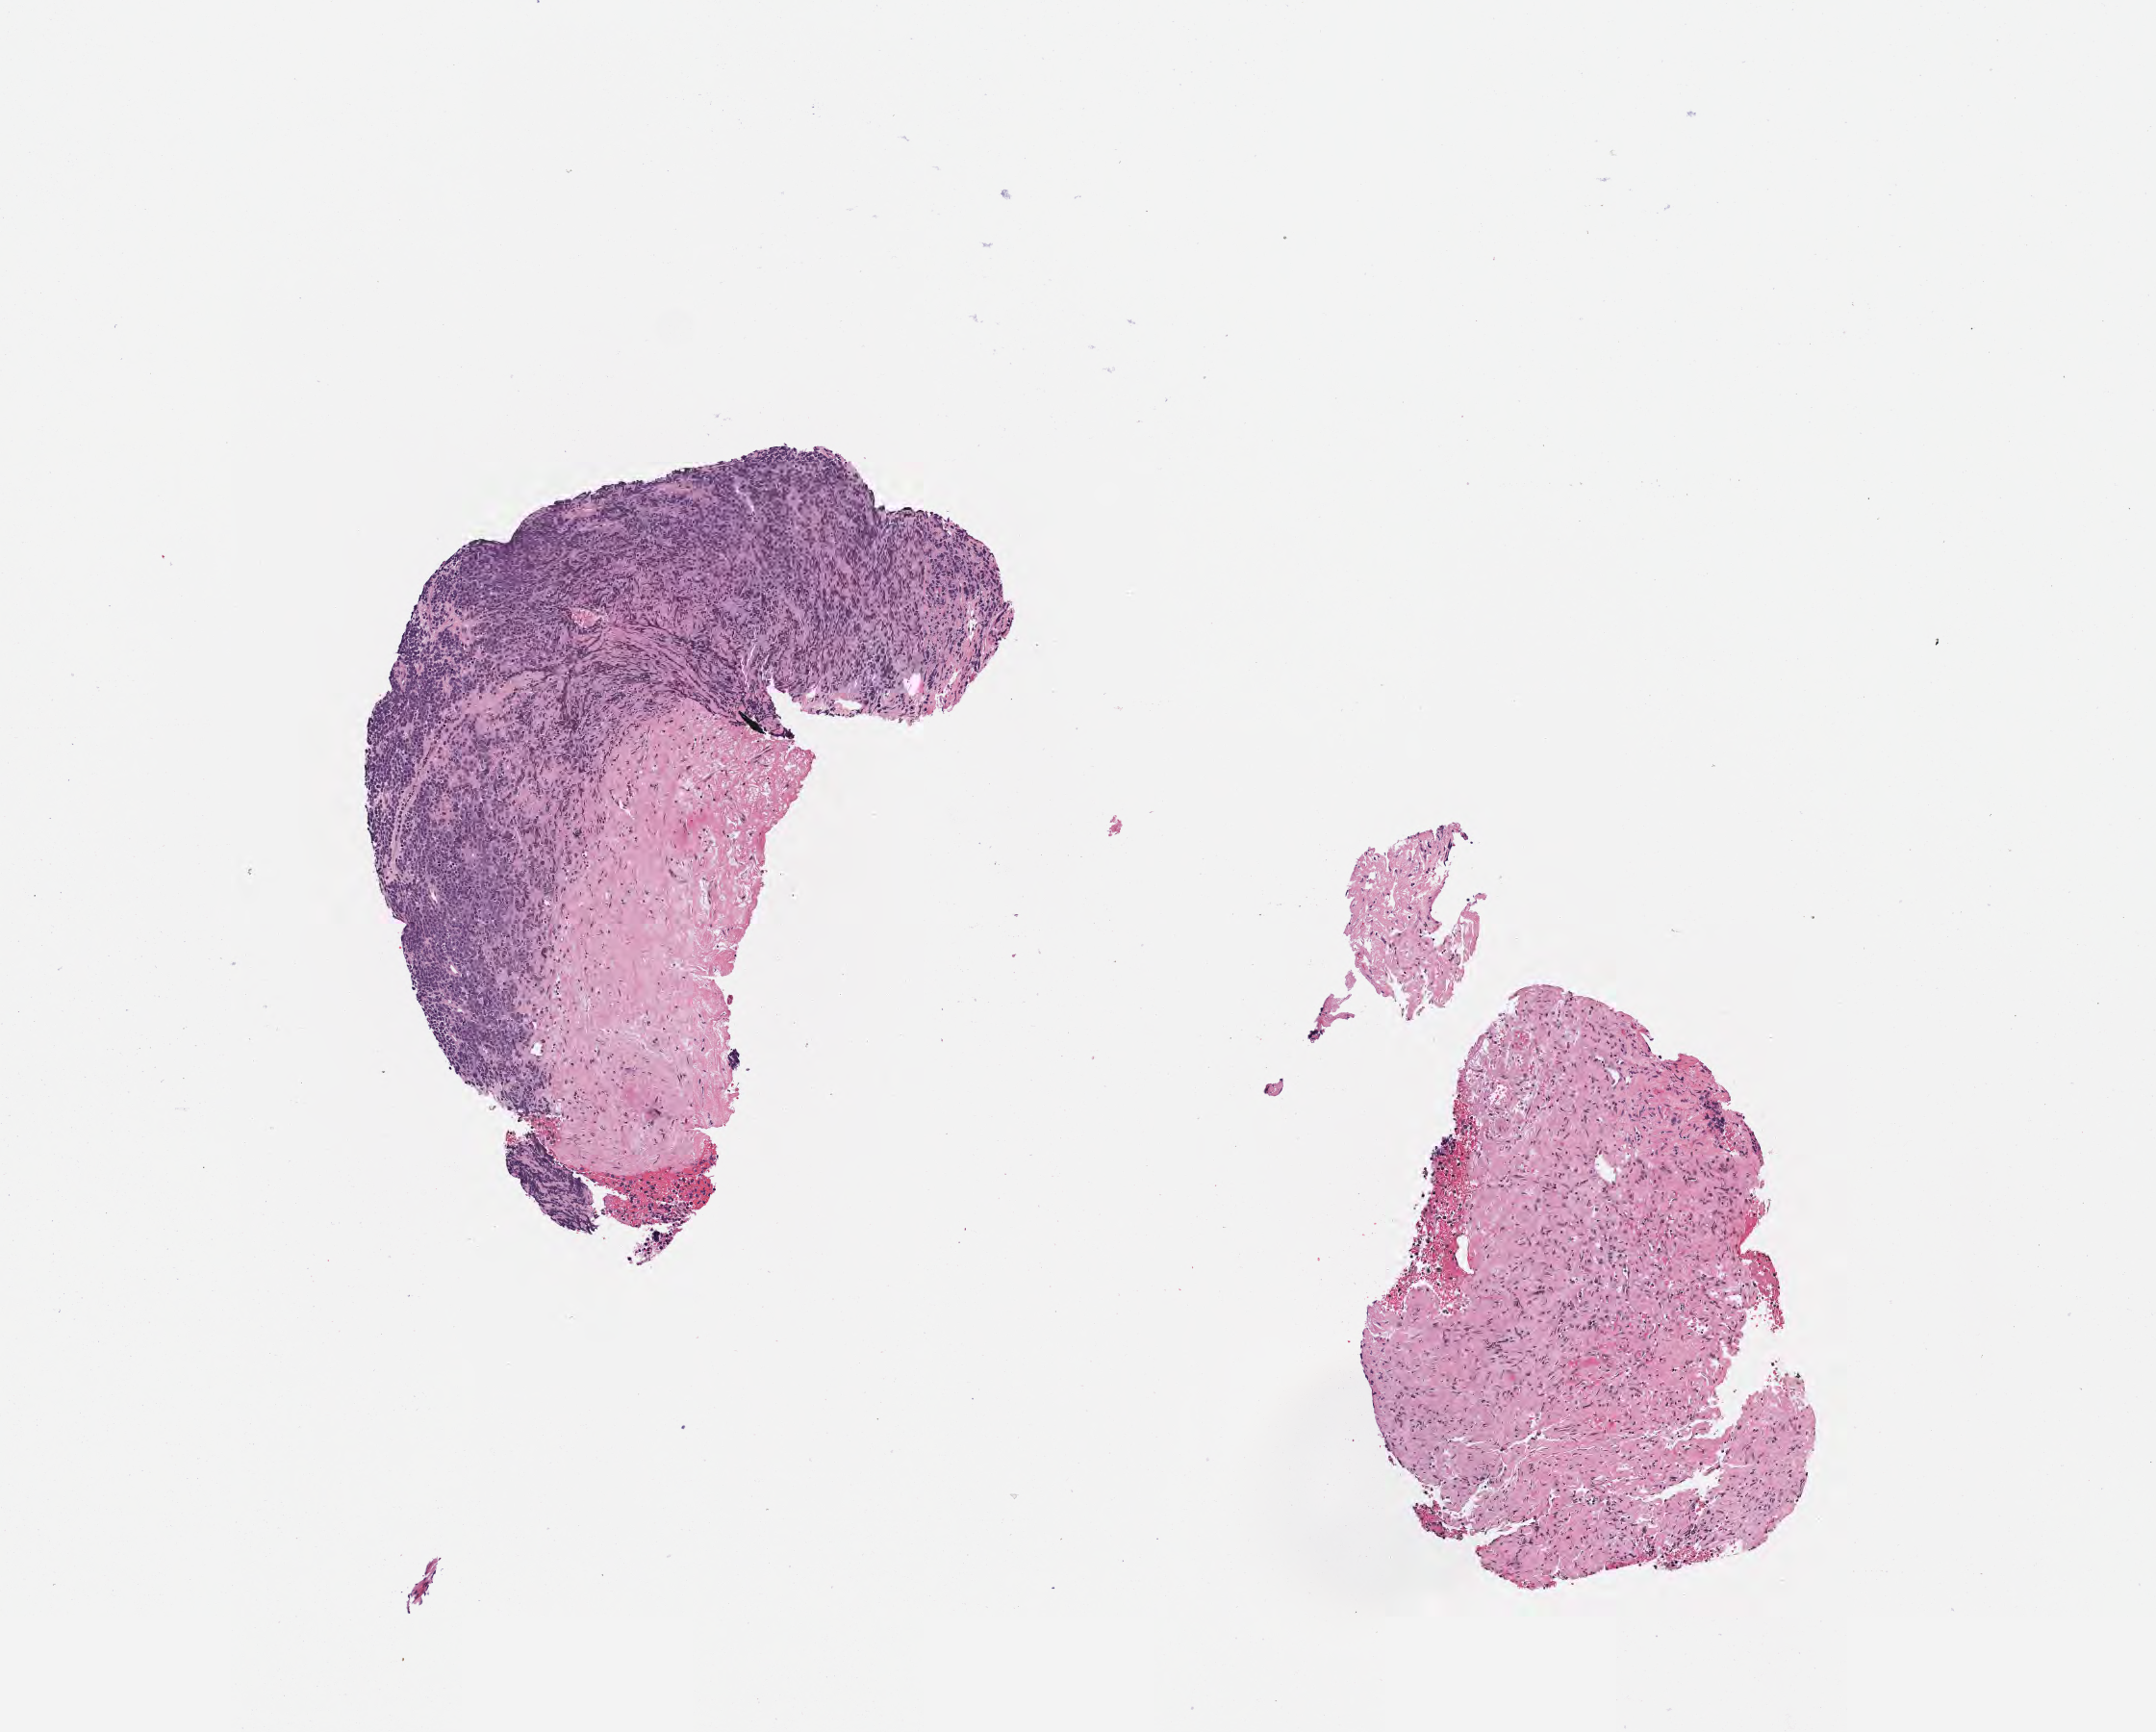
Whole-slide image, hematoxylin and eosin (H&E) stain — a low-resolution overview of the entire scanned area, about 4.5 x 3.6 mm, tumor tissue, site: abdomen proper. Female patient; age at initial diagnosis 6 years.
Diagnosis: Diffuse large B-cell lymphoma, NOS.